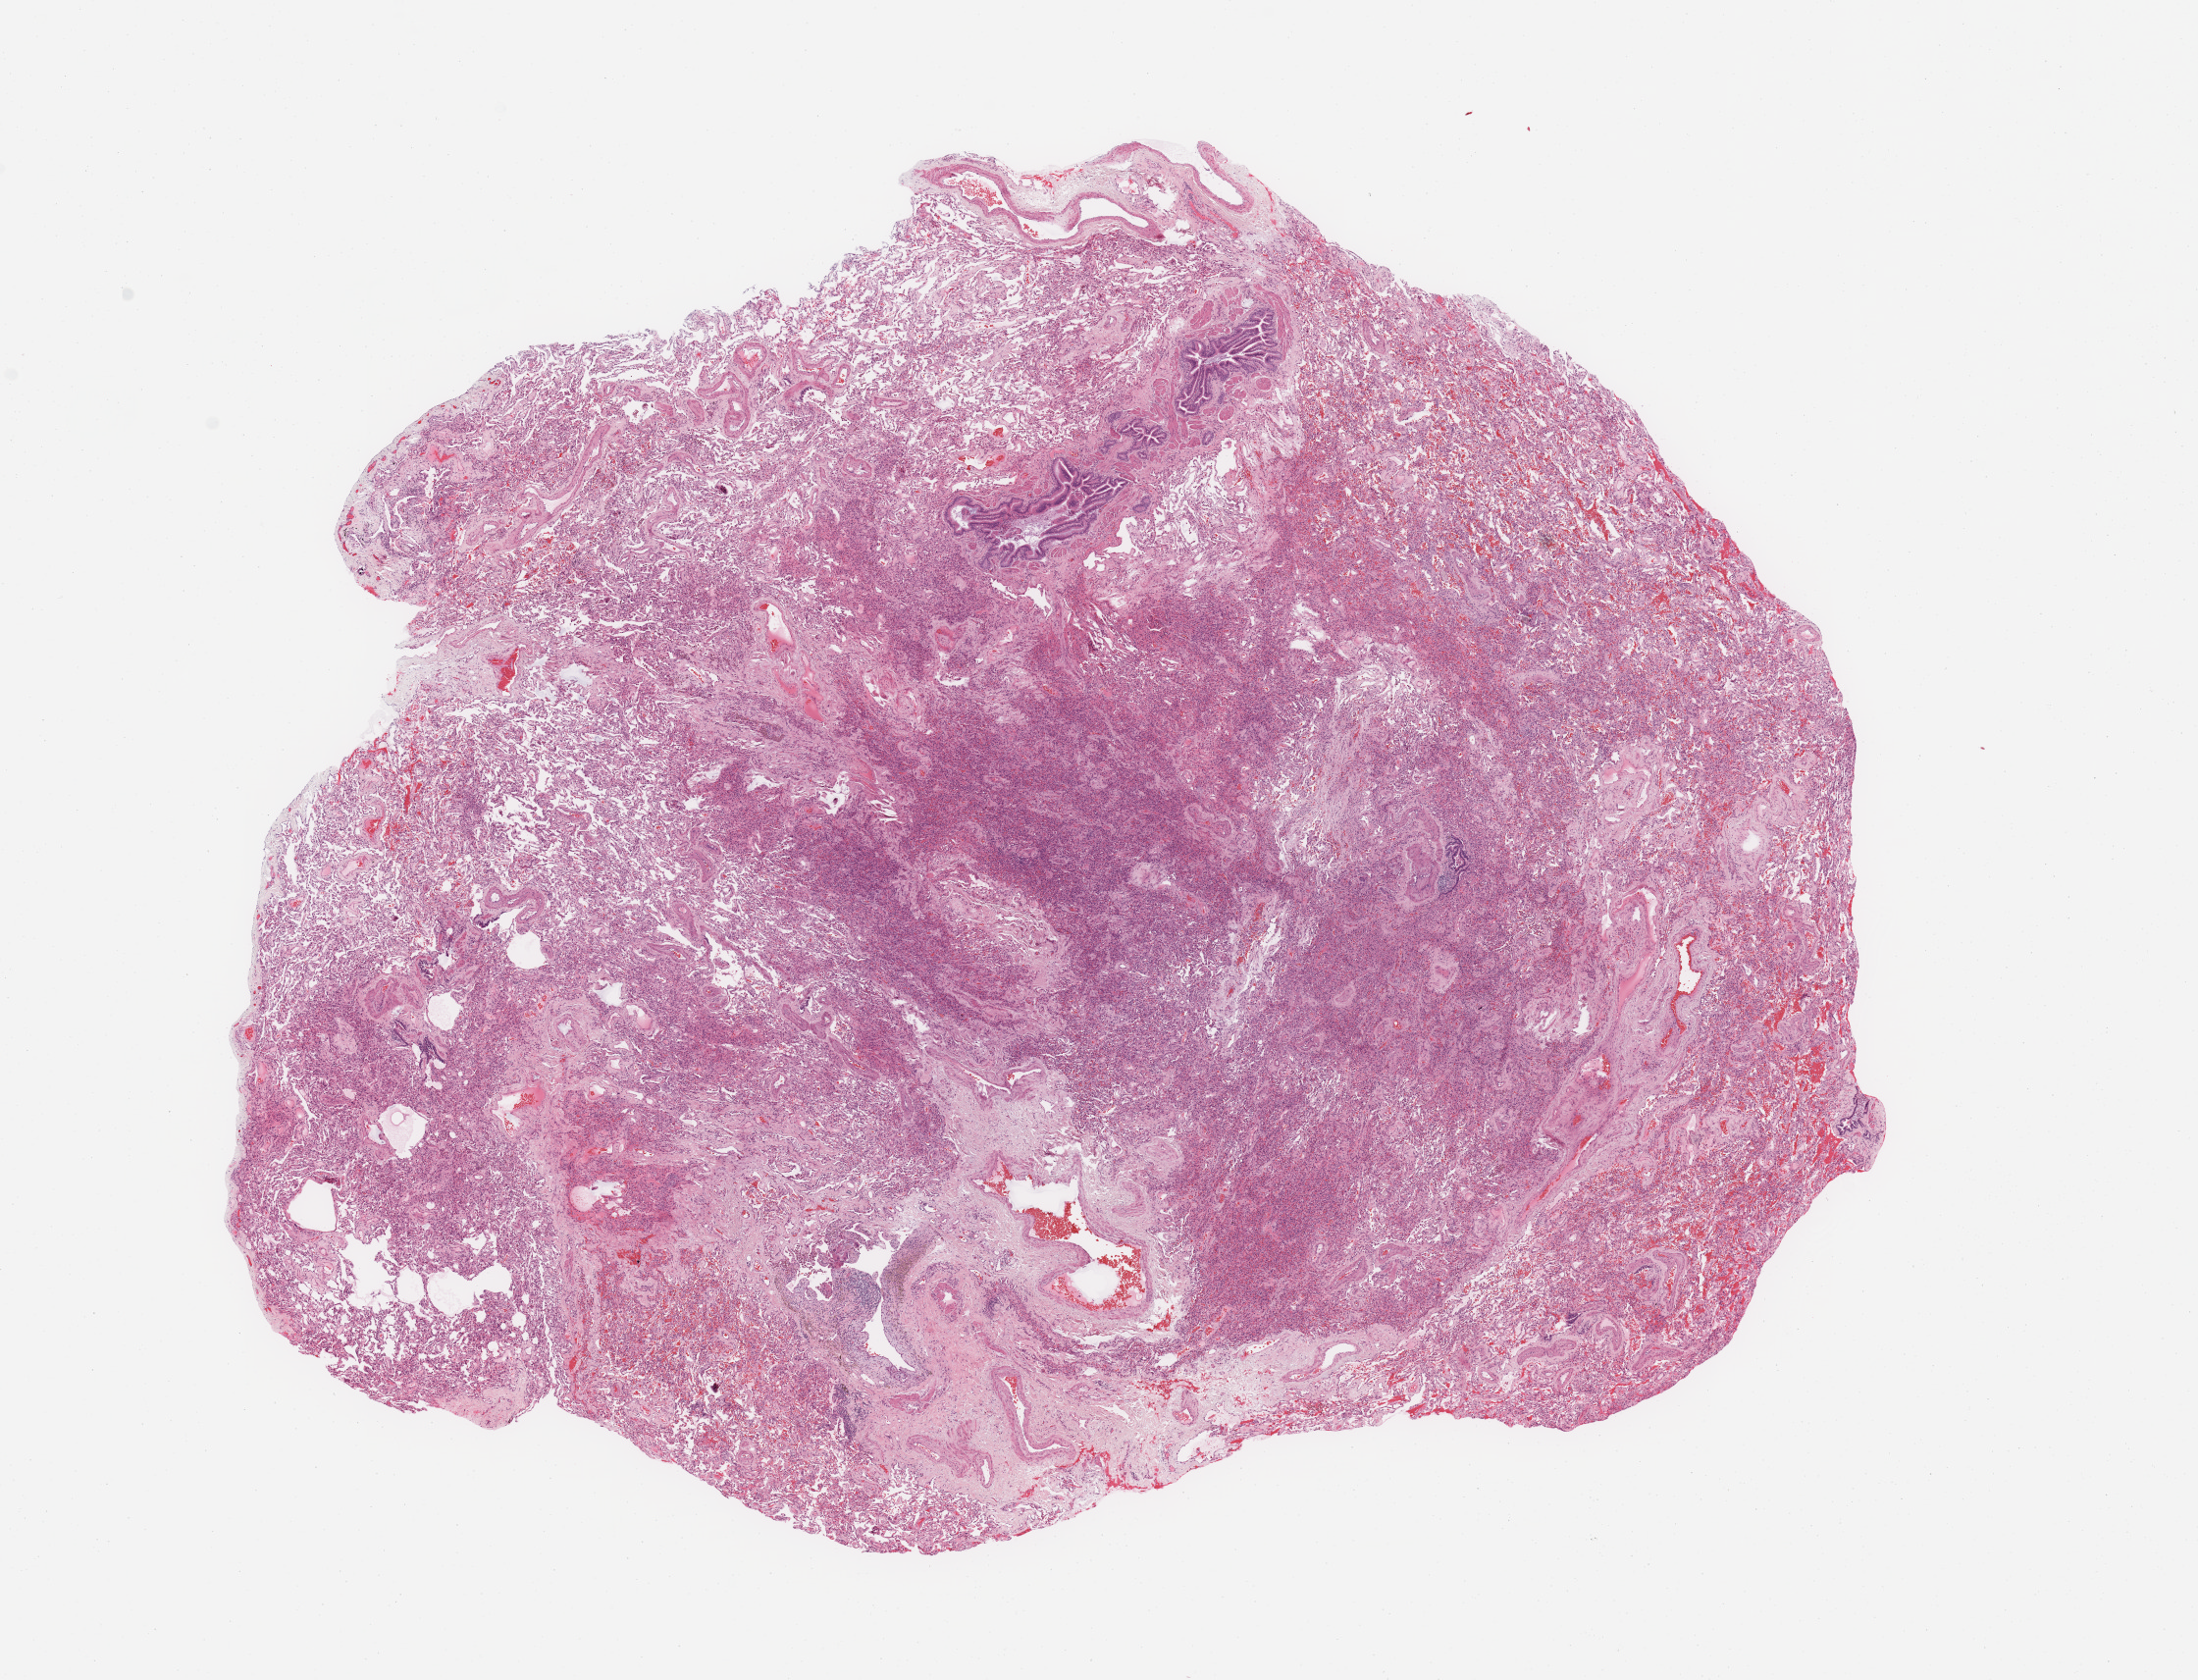
Digitized H&E-stained tissue section (whole slide), whole scanned area (about 17.7 x 13.5 mm, slide scanned at 20x) shown as a low-resolution overview; normal (non-tumour) tissue sample, sampled site: lung. 64-year-old male patient.
This section: normal (non-tumour) tissue from the same patient. Patient diagnosis: Squamous cell carcinoma, NOS.